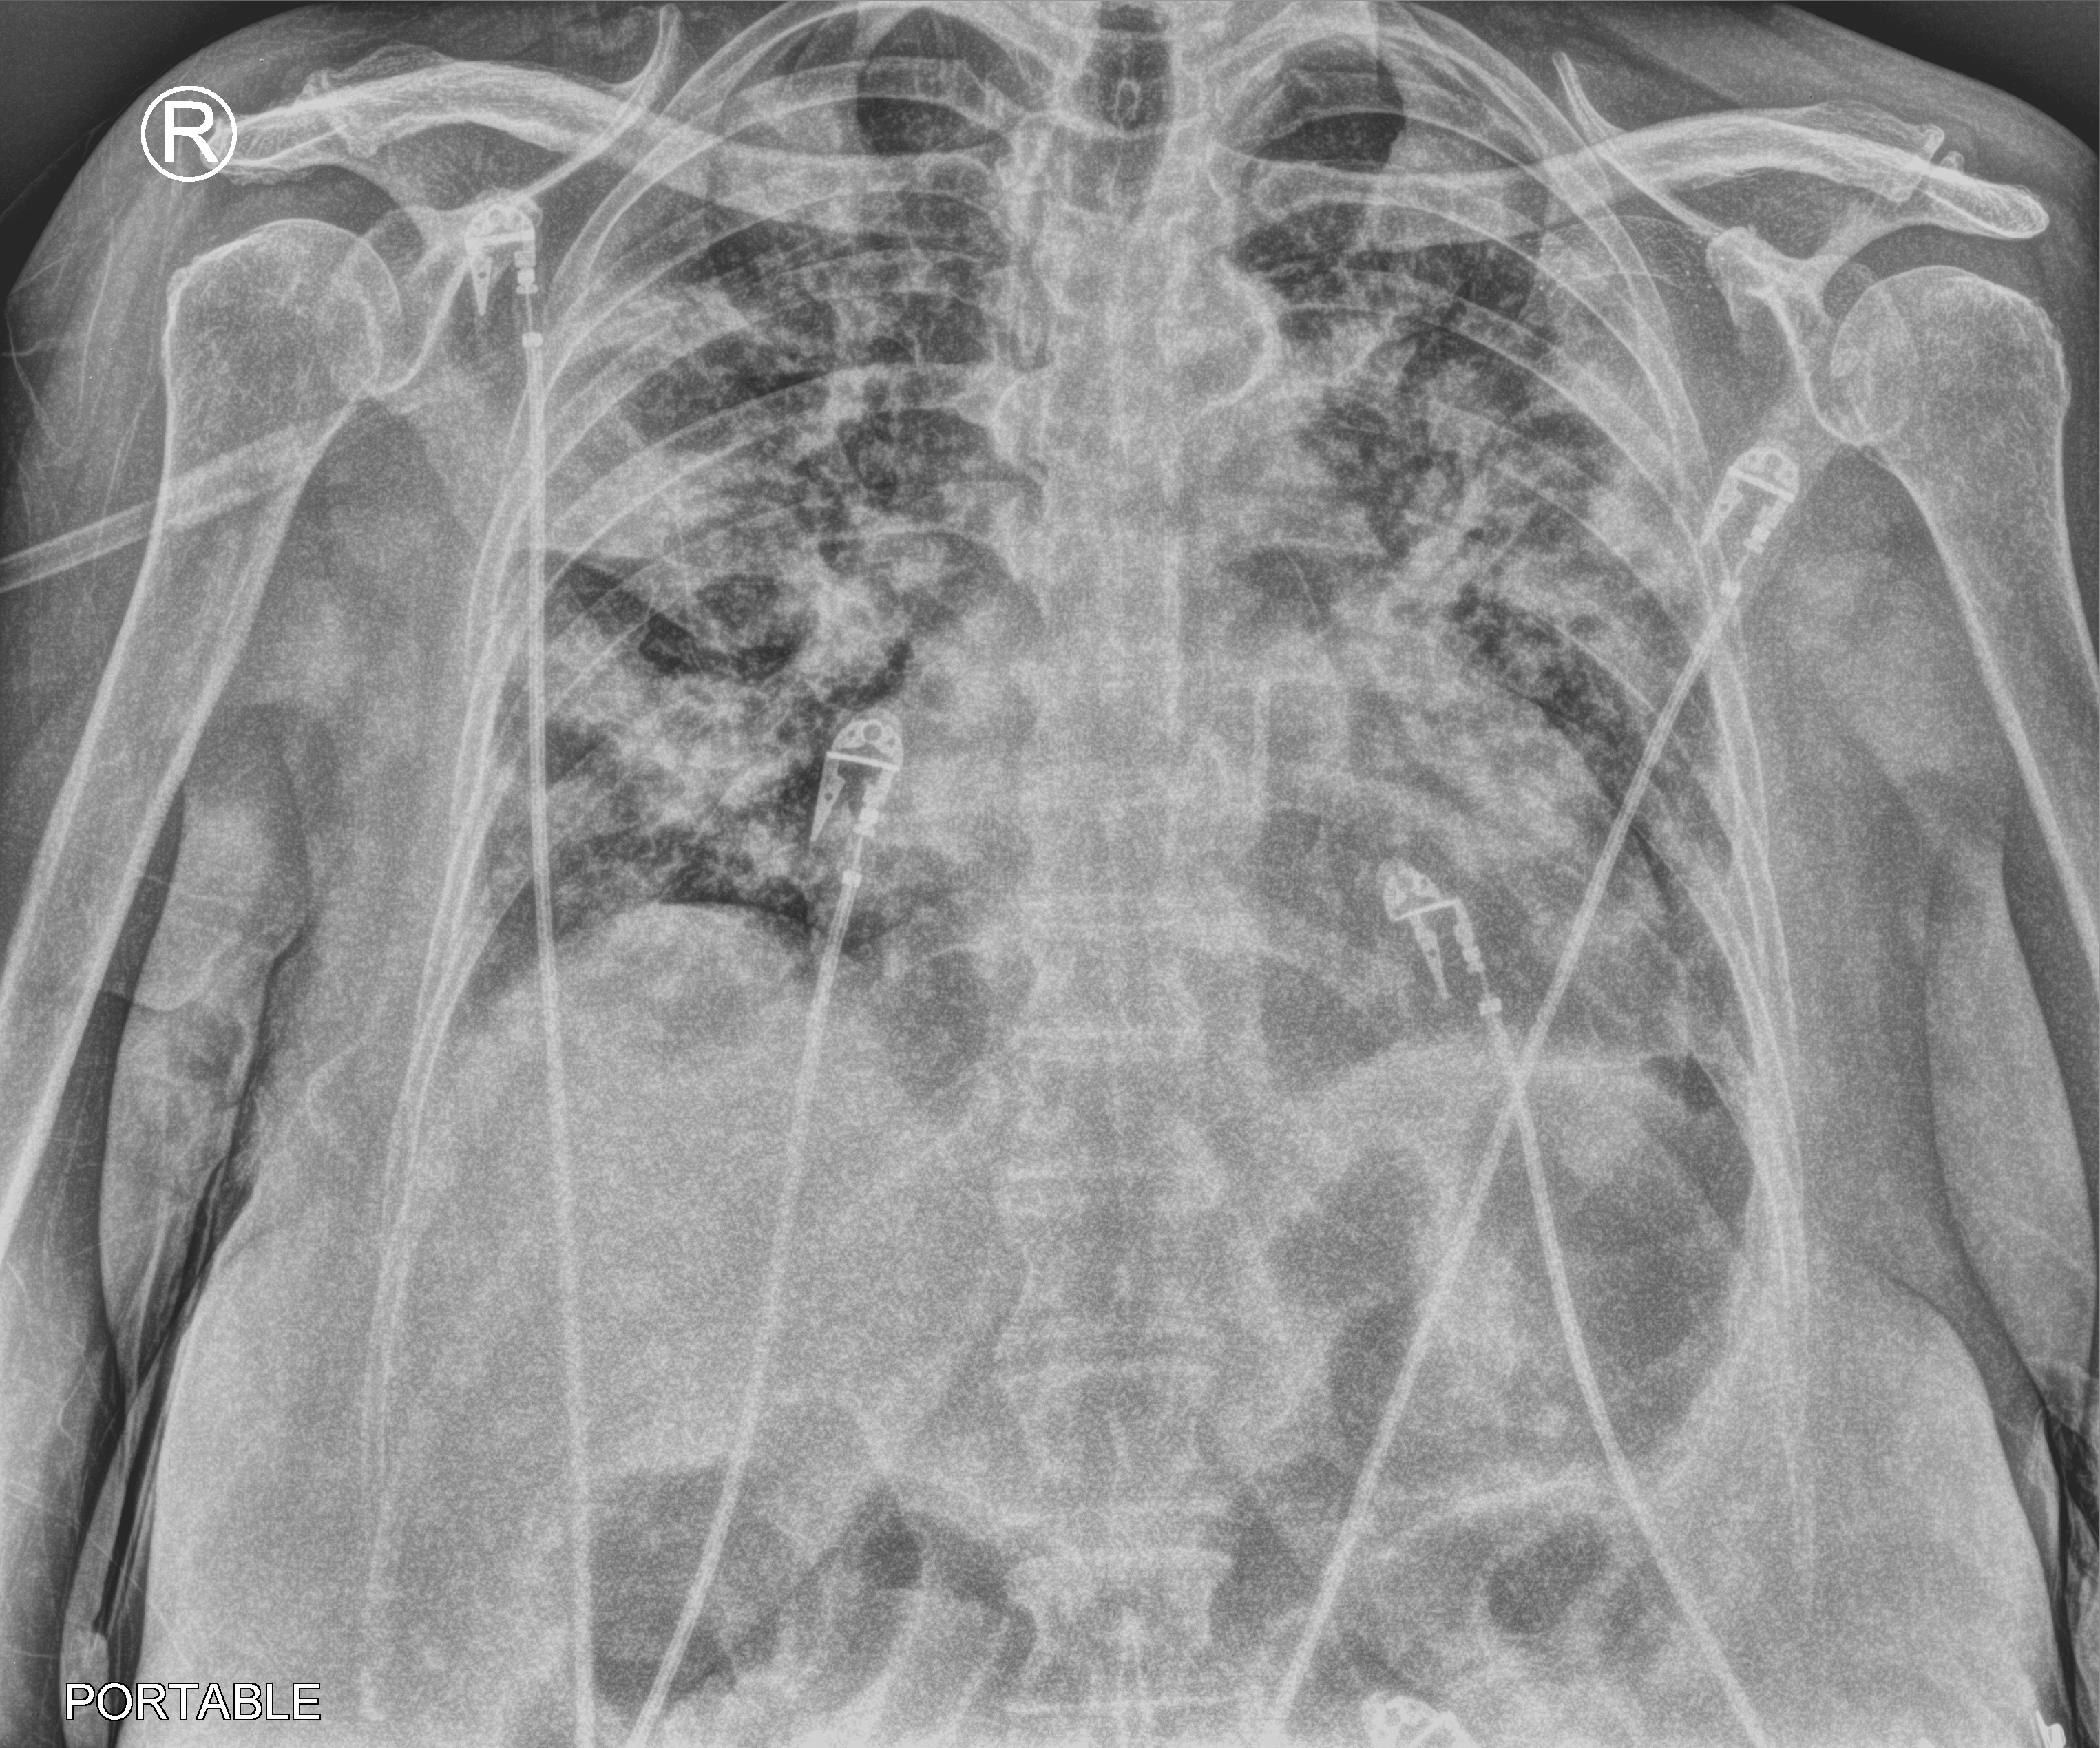
Chest X-ray (portable), anteroposterior (AP) projection. Female patient hospitalised with COVID-19, age 60–74 years.
Hospital-stay facts (about this admission, not read from this image; timing relative to this image not recorded):
- length of hospital stay: 23 days